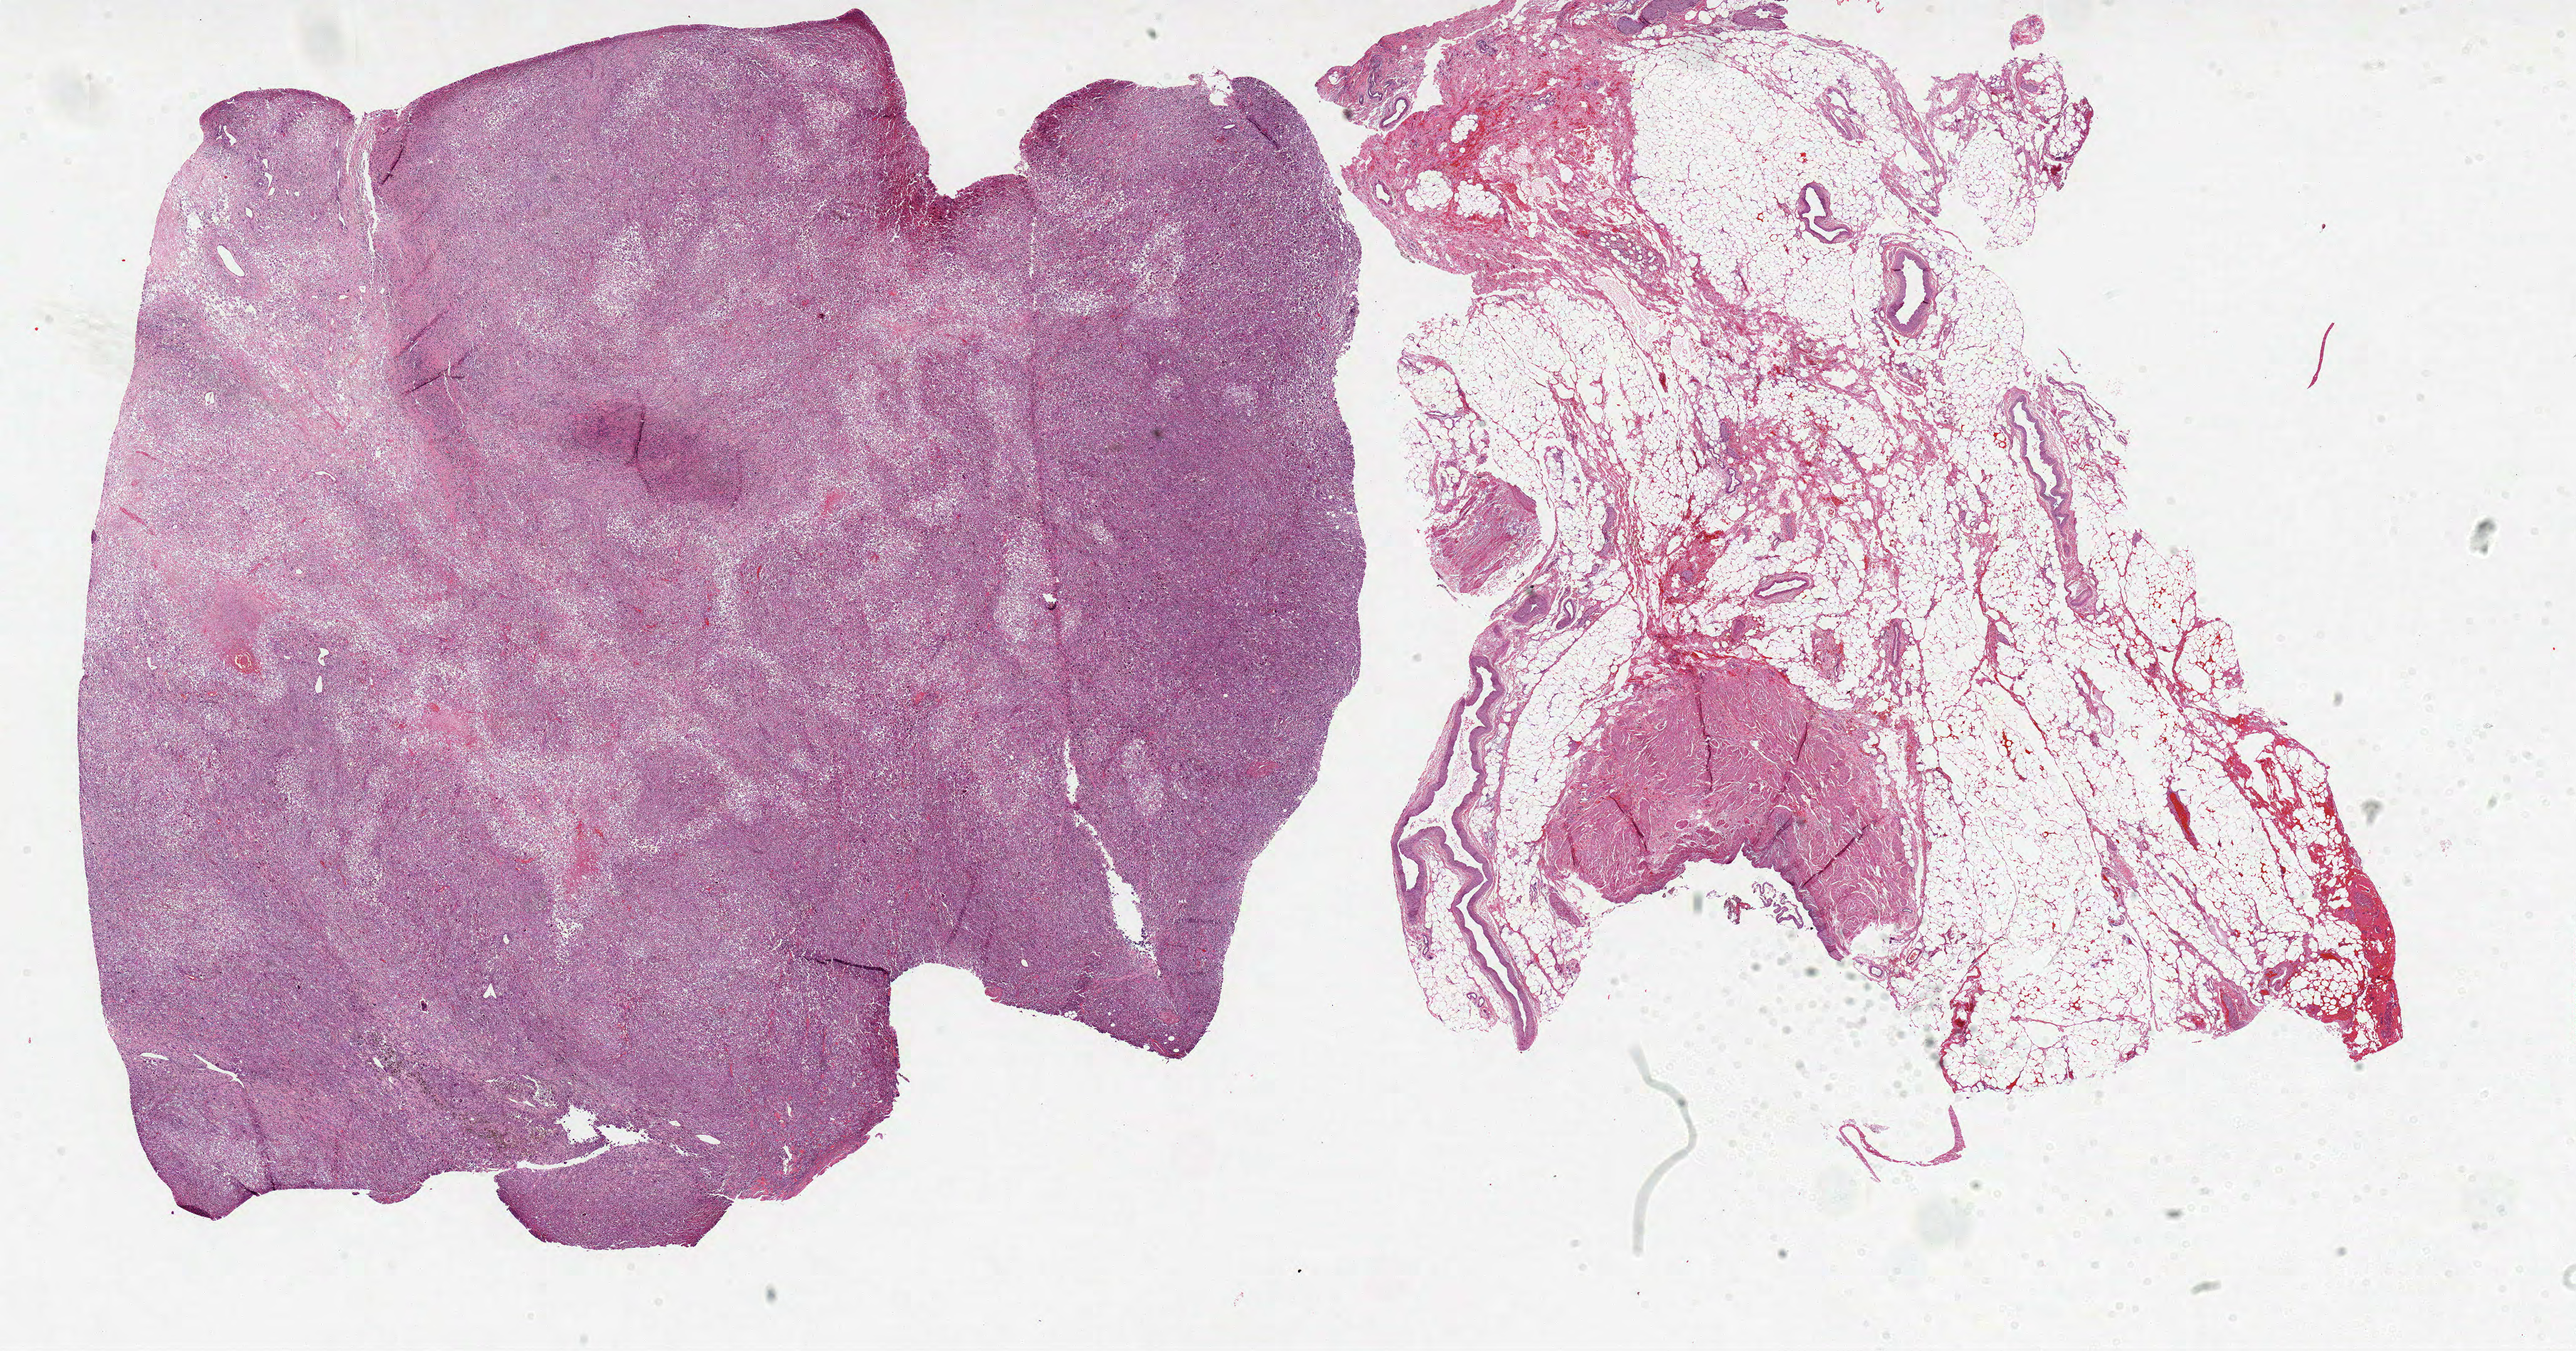
Digitized H&E tissue section (whole slide), whole scanned area (about 28.8 x 15.1 mm) shown as a low-resolution overview, FFPE section, sample: primary tumour, kidney. Female, age 73 years at initial diagnosis. Histologic grade: G4 (undifferentiated).
AJCC pathologic stage: IV. Pathologic diagnosis: Clear cell adenocarcinoma, NOS.